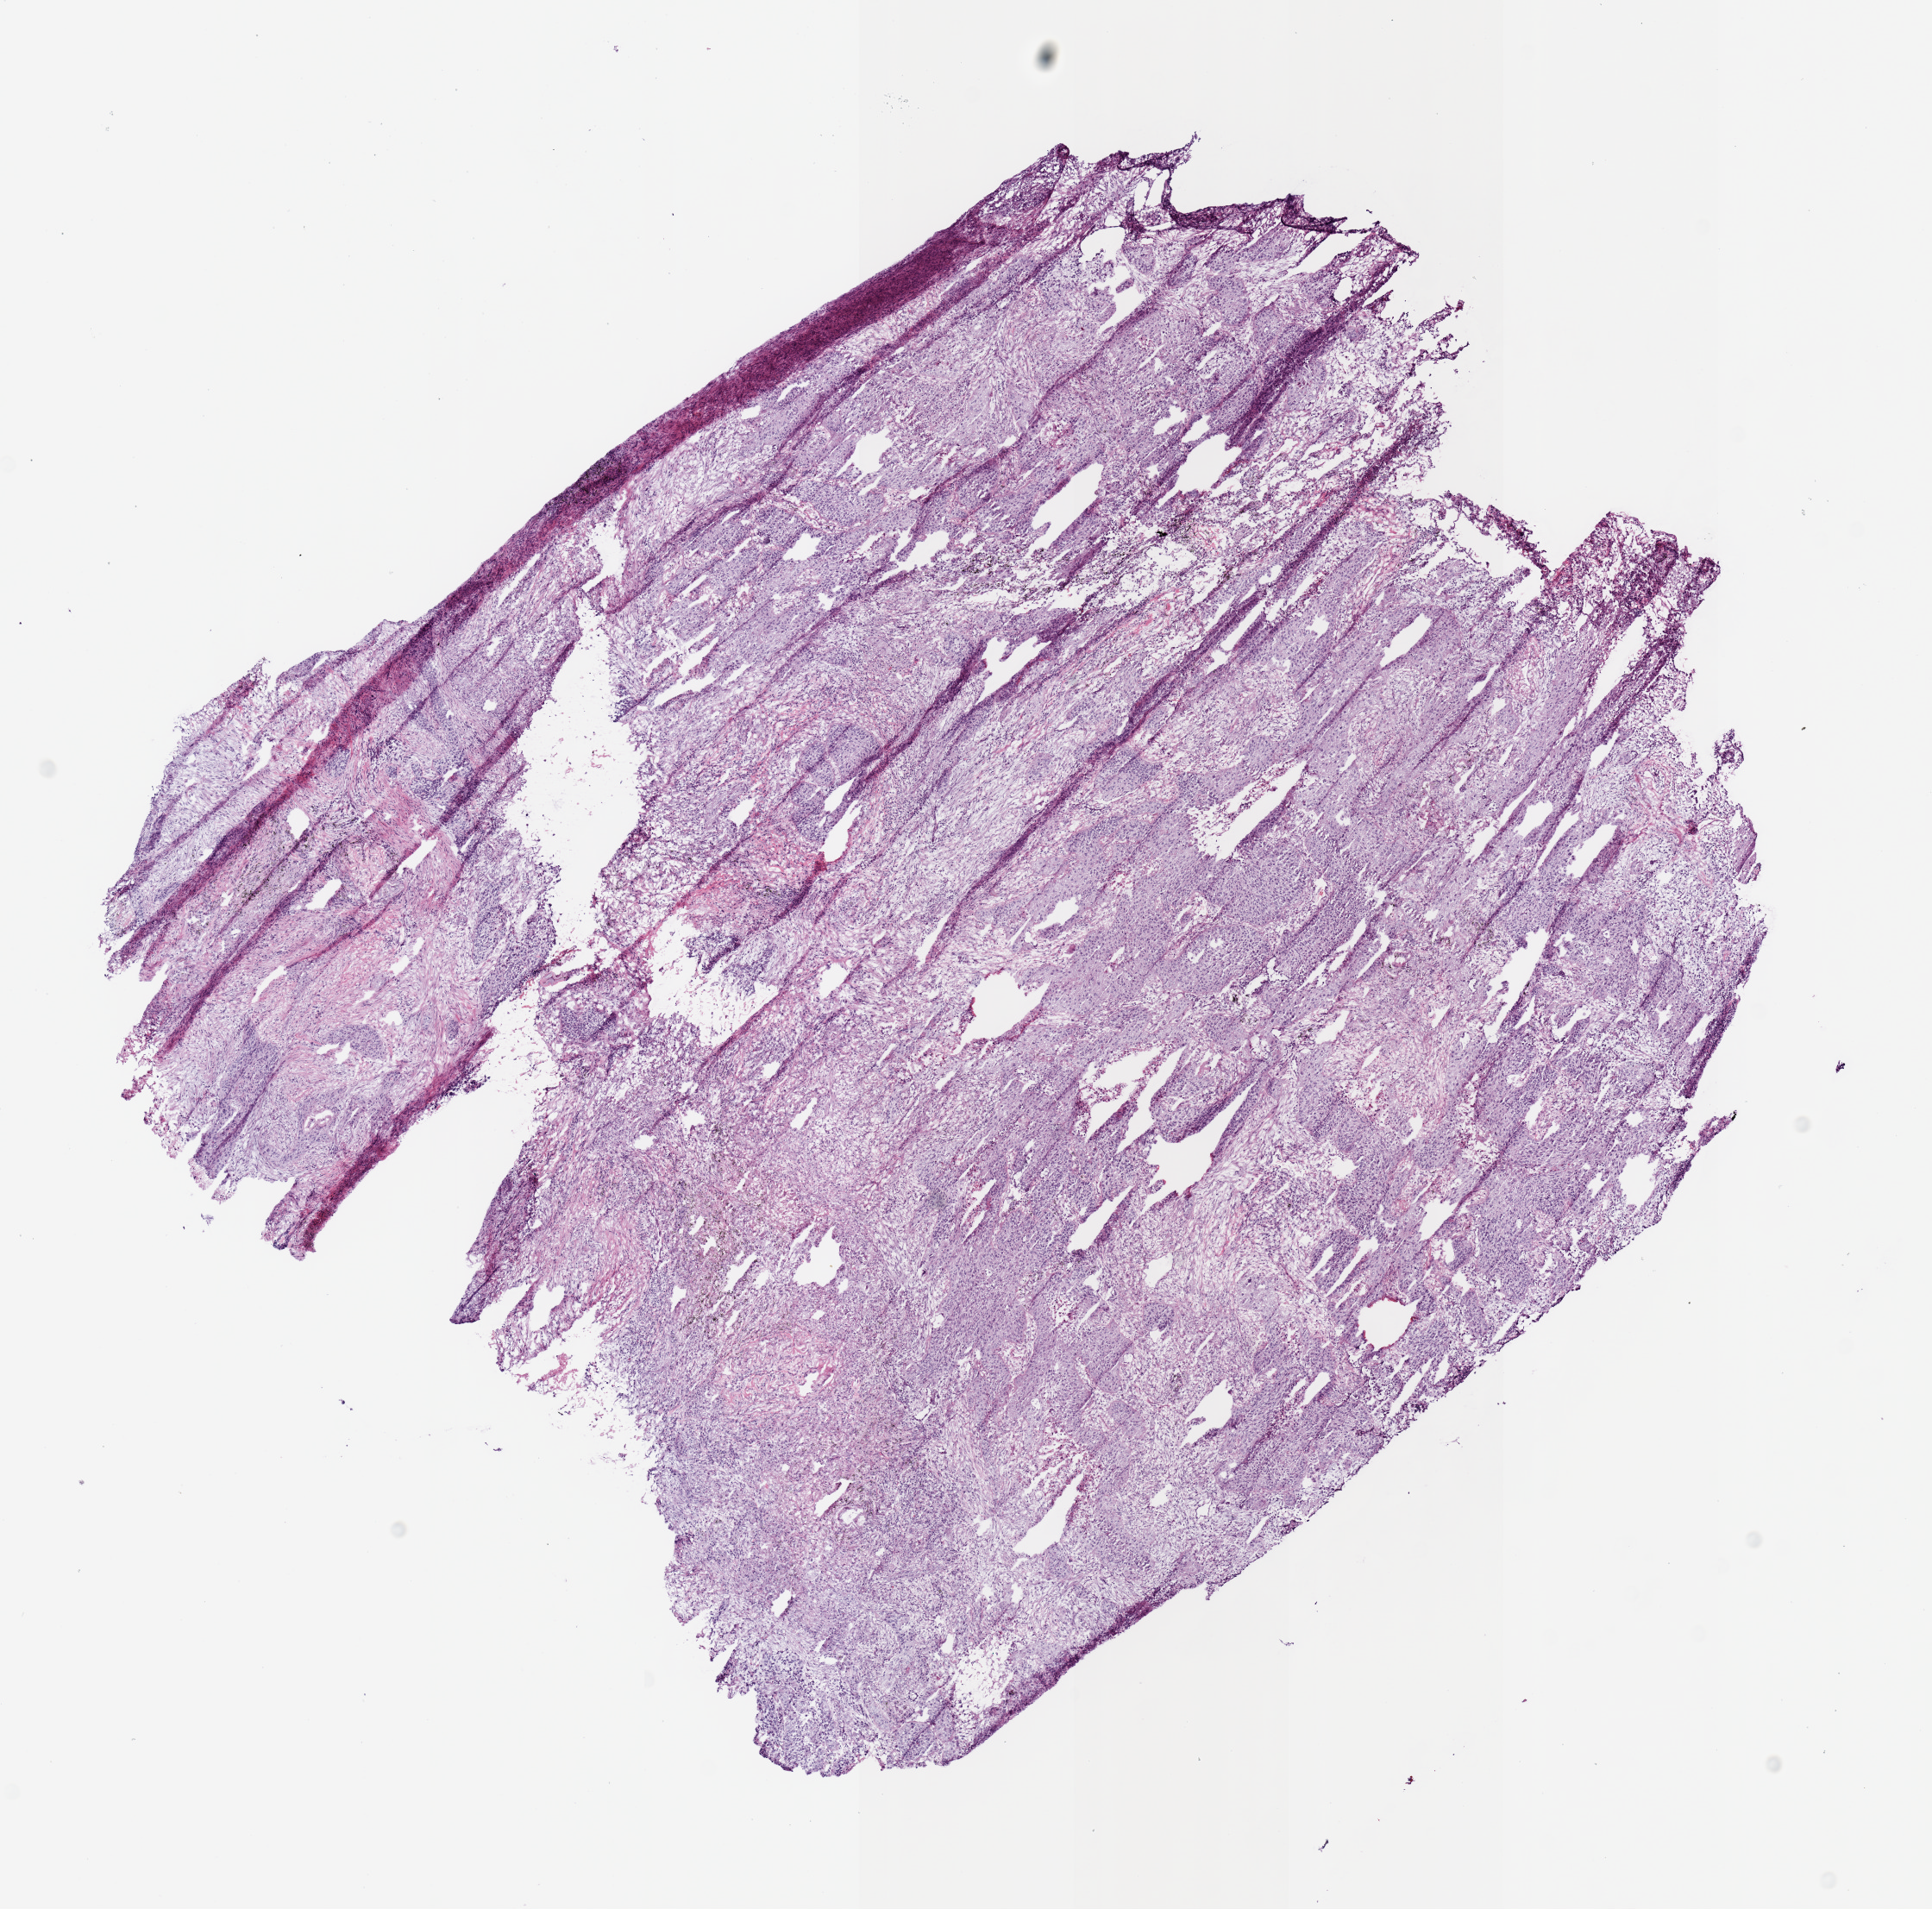
Whole-slide histology image, Hematoxylin and eosin (H&E) stained, low-resolution overview of the scanned area, about 8.9 x 8.7 mm (from a 20x scan); frozen section; sample: primary tumour, lung. Patient: male, age at initial diagnosis 78 years. Composition of this section per pathologist review: tumour cells 100%, tumour nuclei 65%, normal cells 0%, stromal cells 0%, necrosis 0%. Infiltration values recorded for this section: lymphocyte infiltration 25%, monocyte infiltration 2%, neutrophil infiltration 5%.
• pathologic diagnosis: Squamous cell carcinoma, NOS
• laterality: right
• AJCC pathologic stage: IA (7th edition)
• TNM: T1b N0 MX